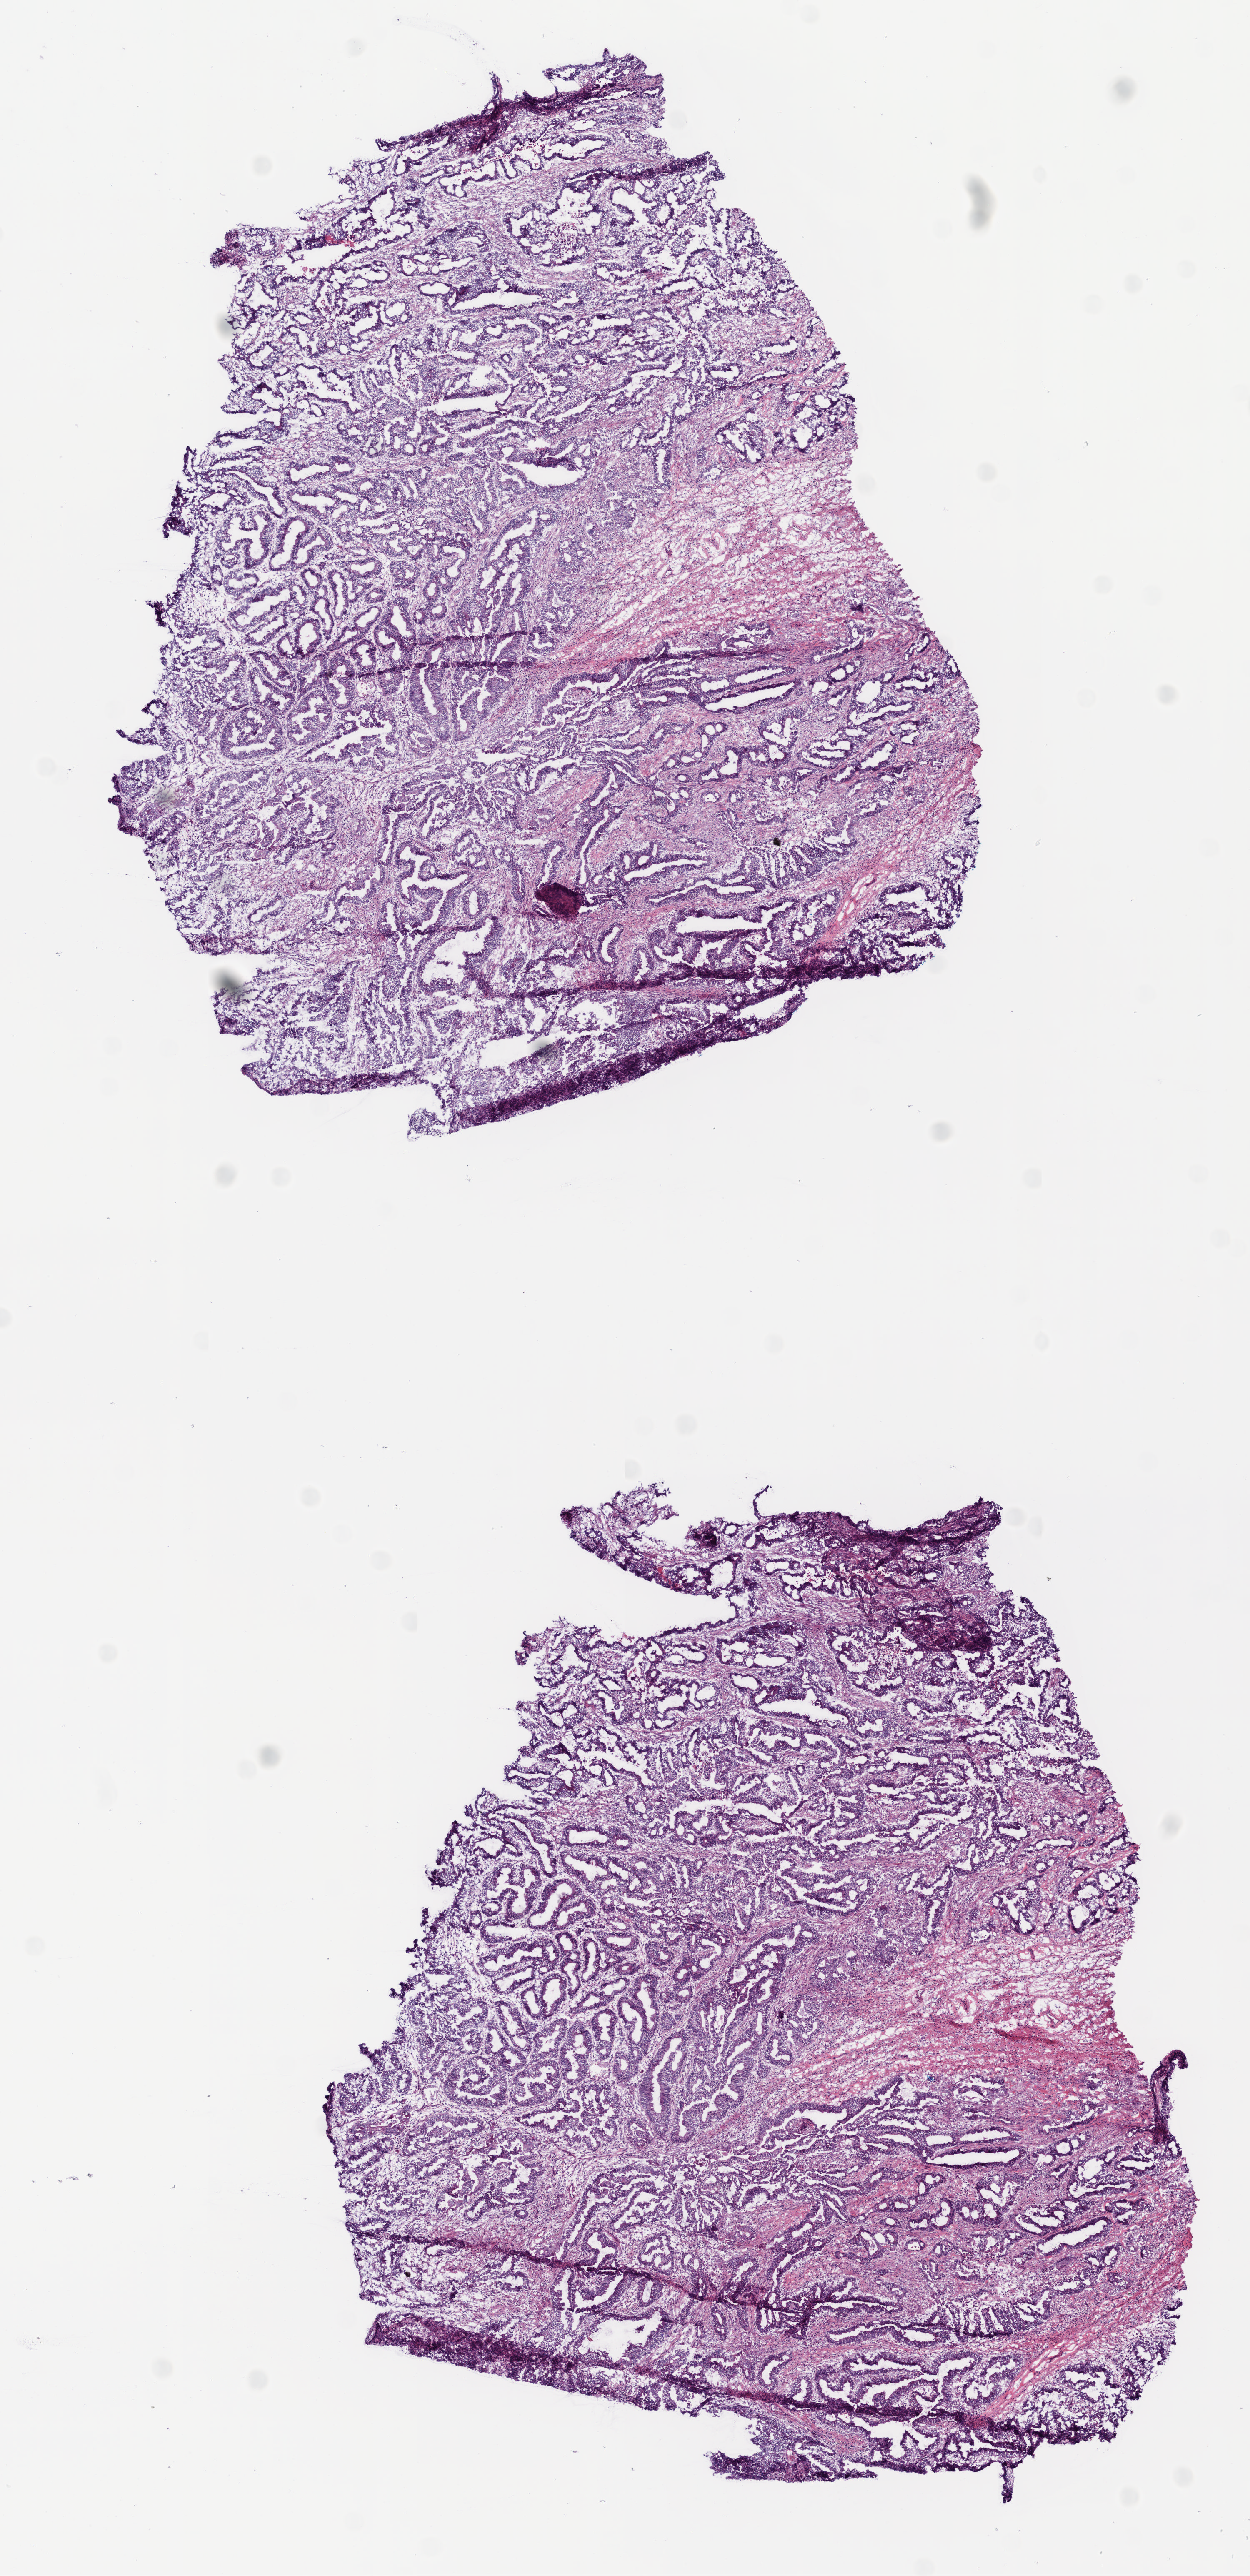
Whole-slide histology image, H&E-stained — whole scanned area (about 6.0 x 12.4 mm, from a 20x scan) shown as a low-resolution overview; frozen section from the top of the tissue portion; rectum, primary tumour sample. Patient: male, age at initial diagnosis 74 years. Slide review estimates, as recorded: tumour cells 75%, tumour nuclei 80%, normal cells 0%, stromal cells 20%, necrosis 5%.
AJCC pathologic stage: IIIB (6th edition). Pathologic diagnosis: Adenocarcinoma, NOS (rectosigmoid junction).